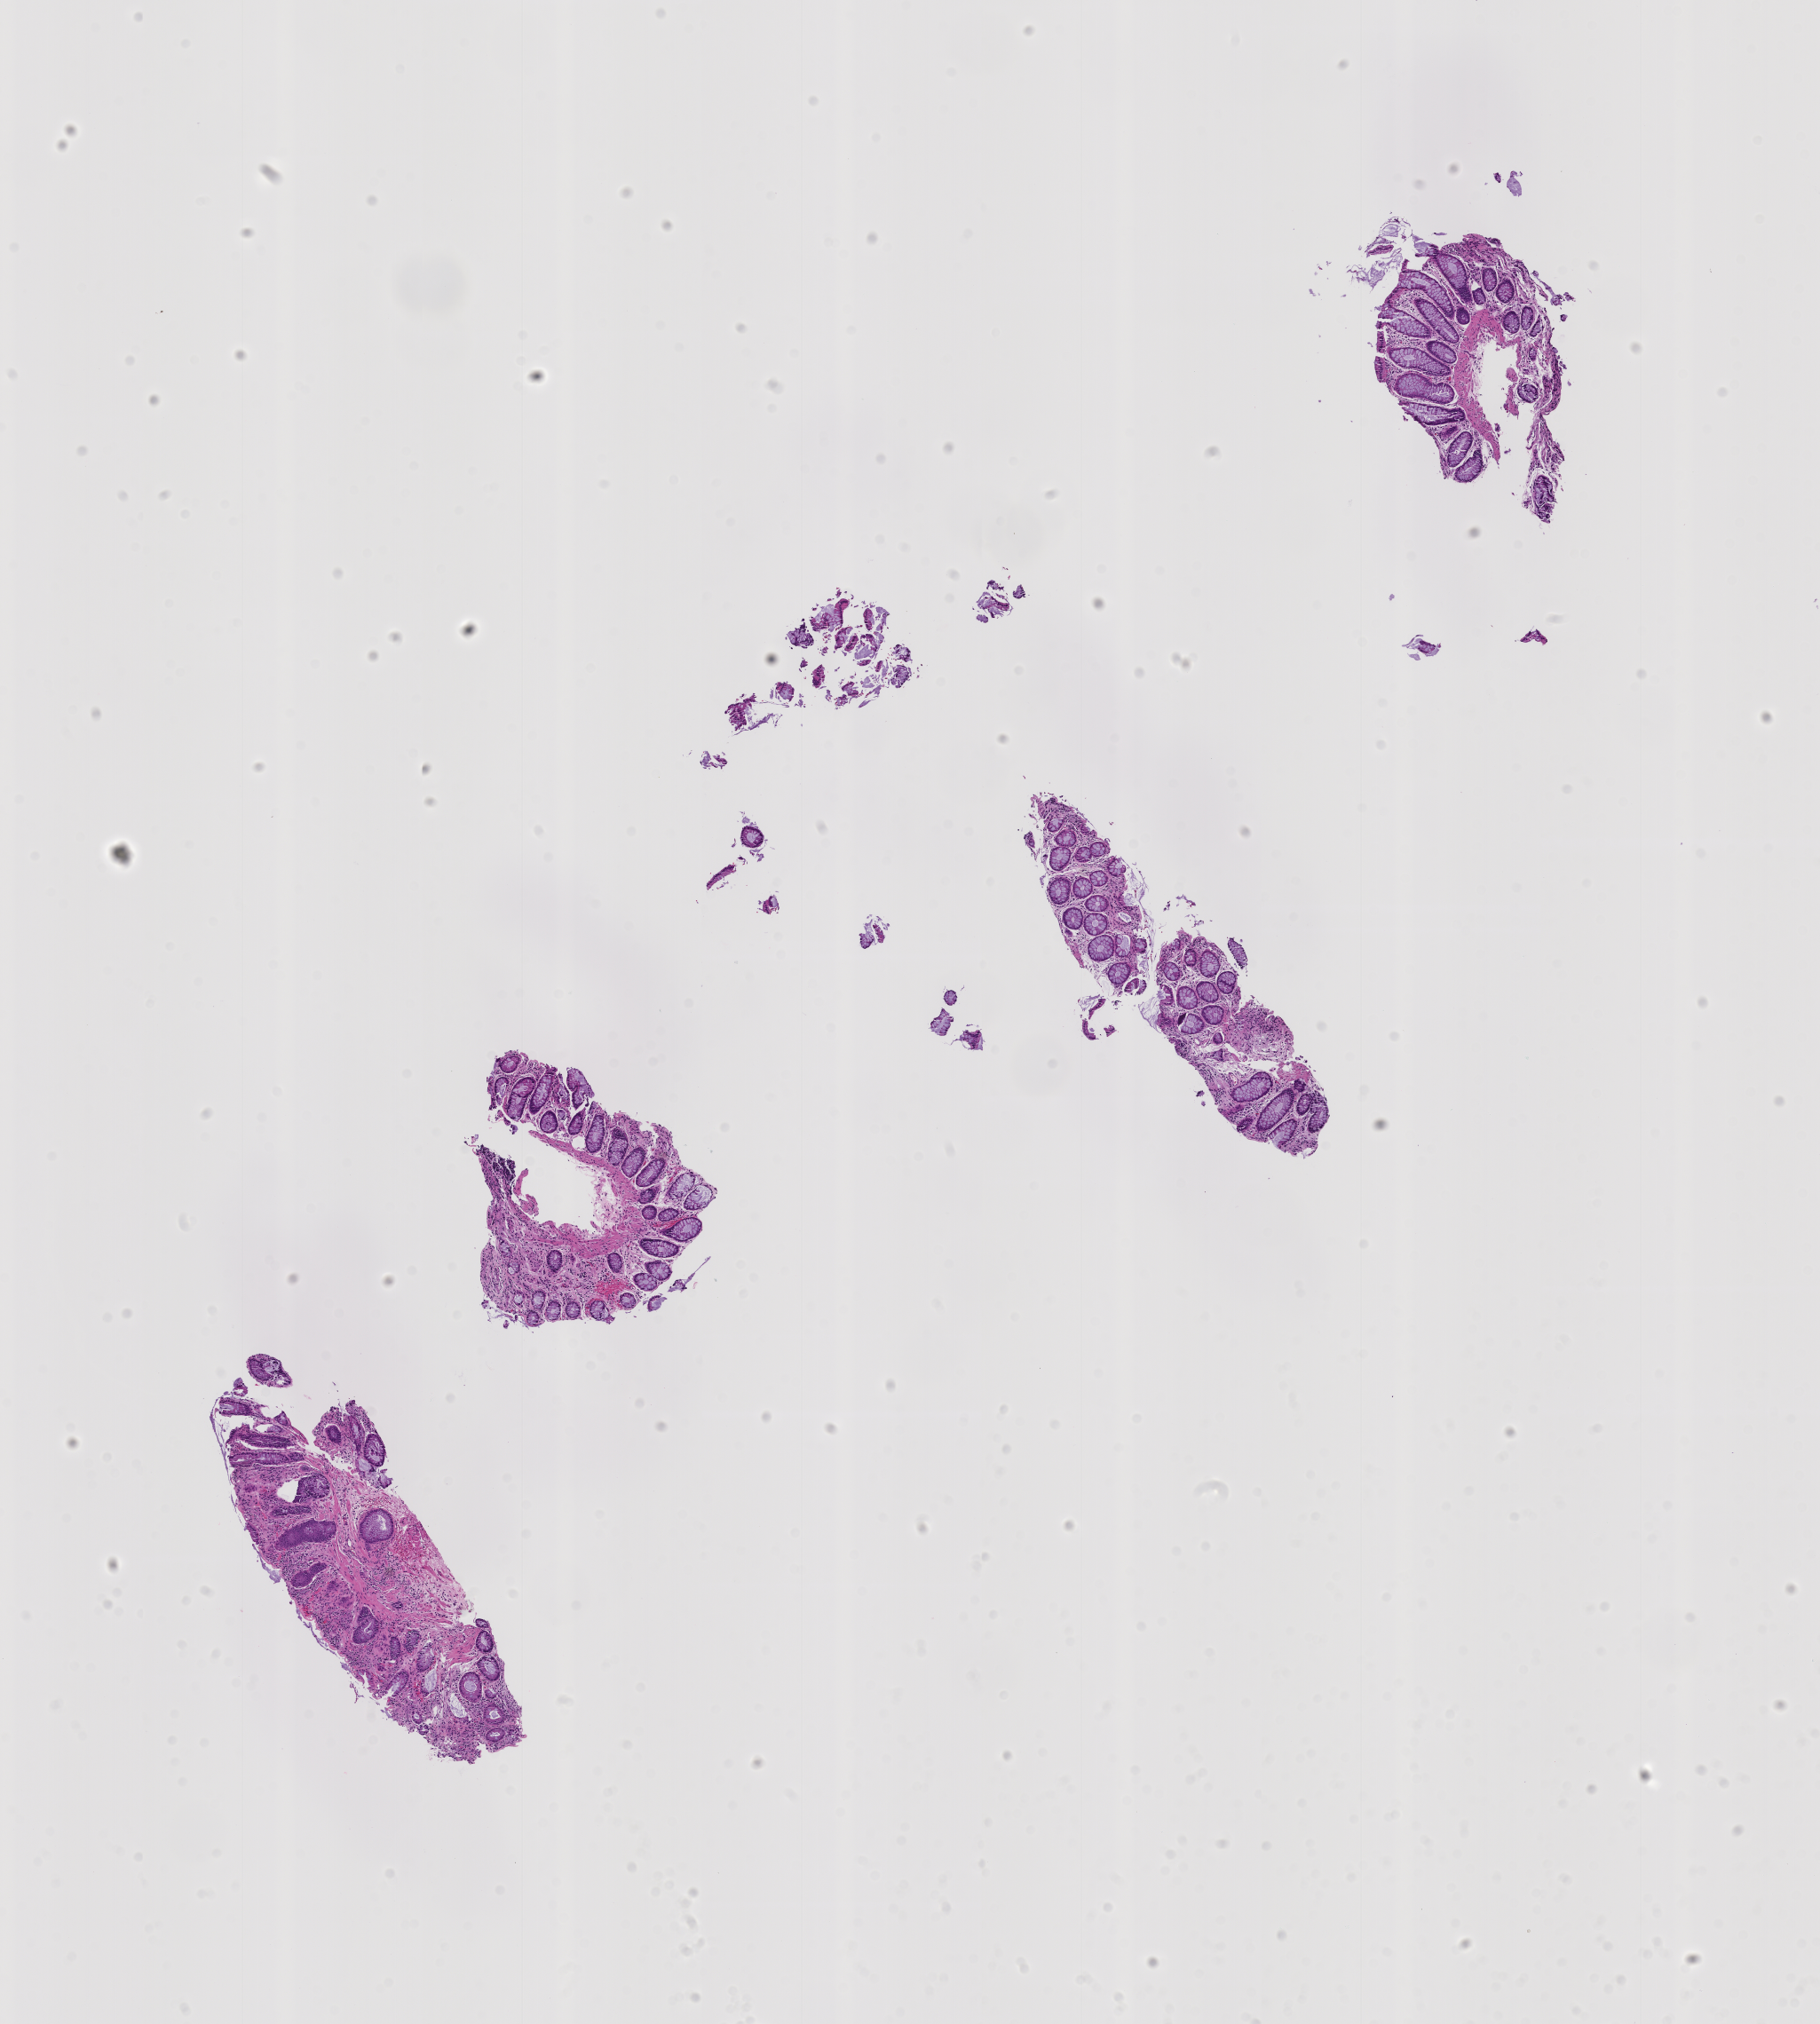
Whole-slide image, haematoxylin and eosin stain: colon biopsy — whole scanned area (about 8.2 x 9.1 mm) shown as a low-resolution overview; formalin-fixed, paraffin-embedded (FFPE) tissue; site: sigmoid colon. Patient sex: female.
Lesion category (as recorded): hyperplasia.